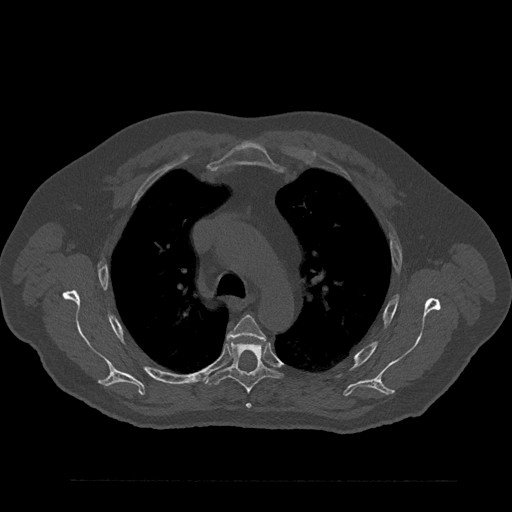
CT including the spine, one axial slice; reconstruction kernel Br40s/3; bone window (W 1800 / L 400 HU); 0.5 mm slice thickness; 512 × 512 image matrix. Patient: male, 61 years. Case-level facts recorded for this patient, not image findings: primary cancer: prostate.
Annotated regions visible in this slice (semi-automatically segmented with operator editing):
- T4 vertebra: bounding box <227,315,266,409> (left, top, right, bottom; pixels)
- T5 vertebra: <205,341,280,394>